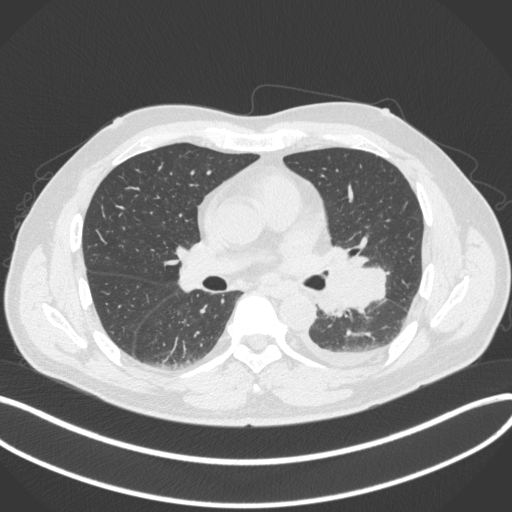
Chest CT, one axial slice. Slice 195 of 350 in the series (ordered by position). Reconstruction kernel B31f. 120 kVp. Lung window (W 1500 / L -600 HU). 1 mm slice thickness. 512 × 512 image matrix, field of view 400 × 400 mm. Patient: male, 58 years. Case-level facts recorded for this patient, not image findings: clinical TNM (as recorded): T3 N1 M1b; histopathological grade: G3.
Structures marked on this image (bounding box drawn by a radiologist):
- lung tumour (recorded histology: small cell carcinoma): bounding box (x1, y1, x2, y2) in pixels: (313, 254, 389, 319)